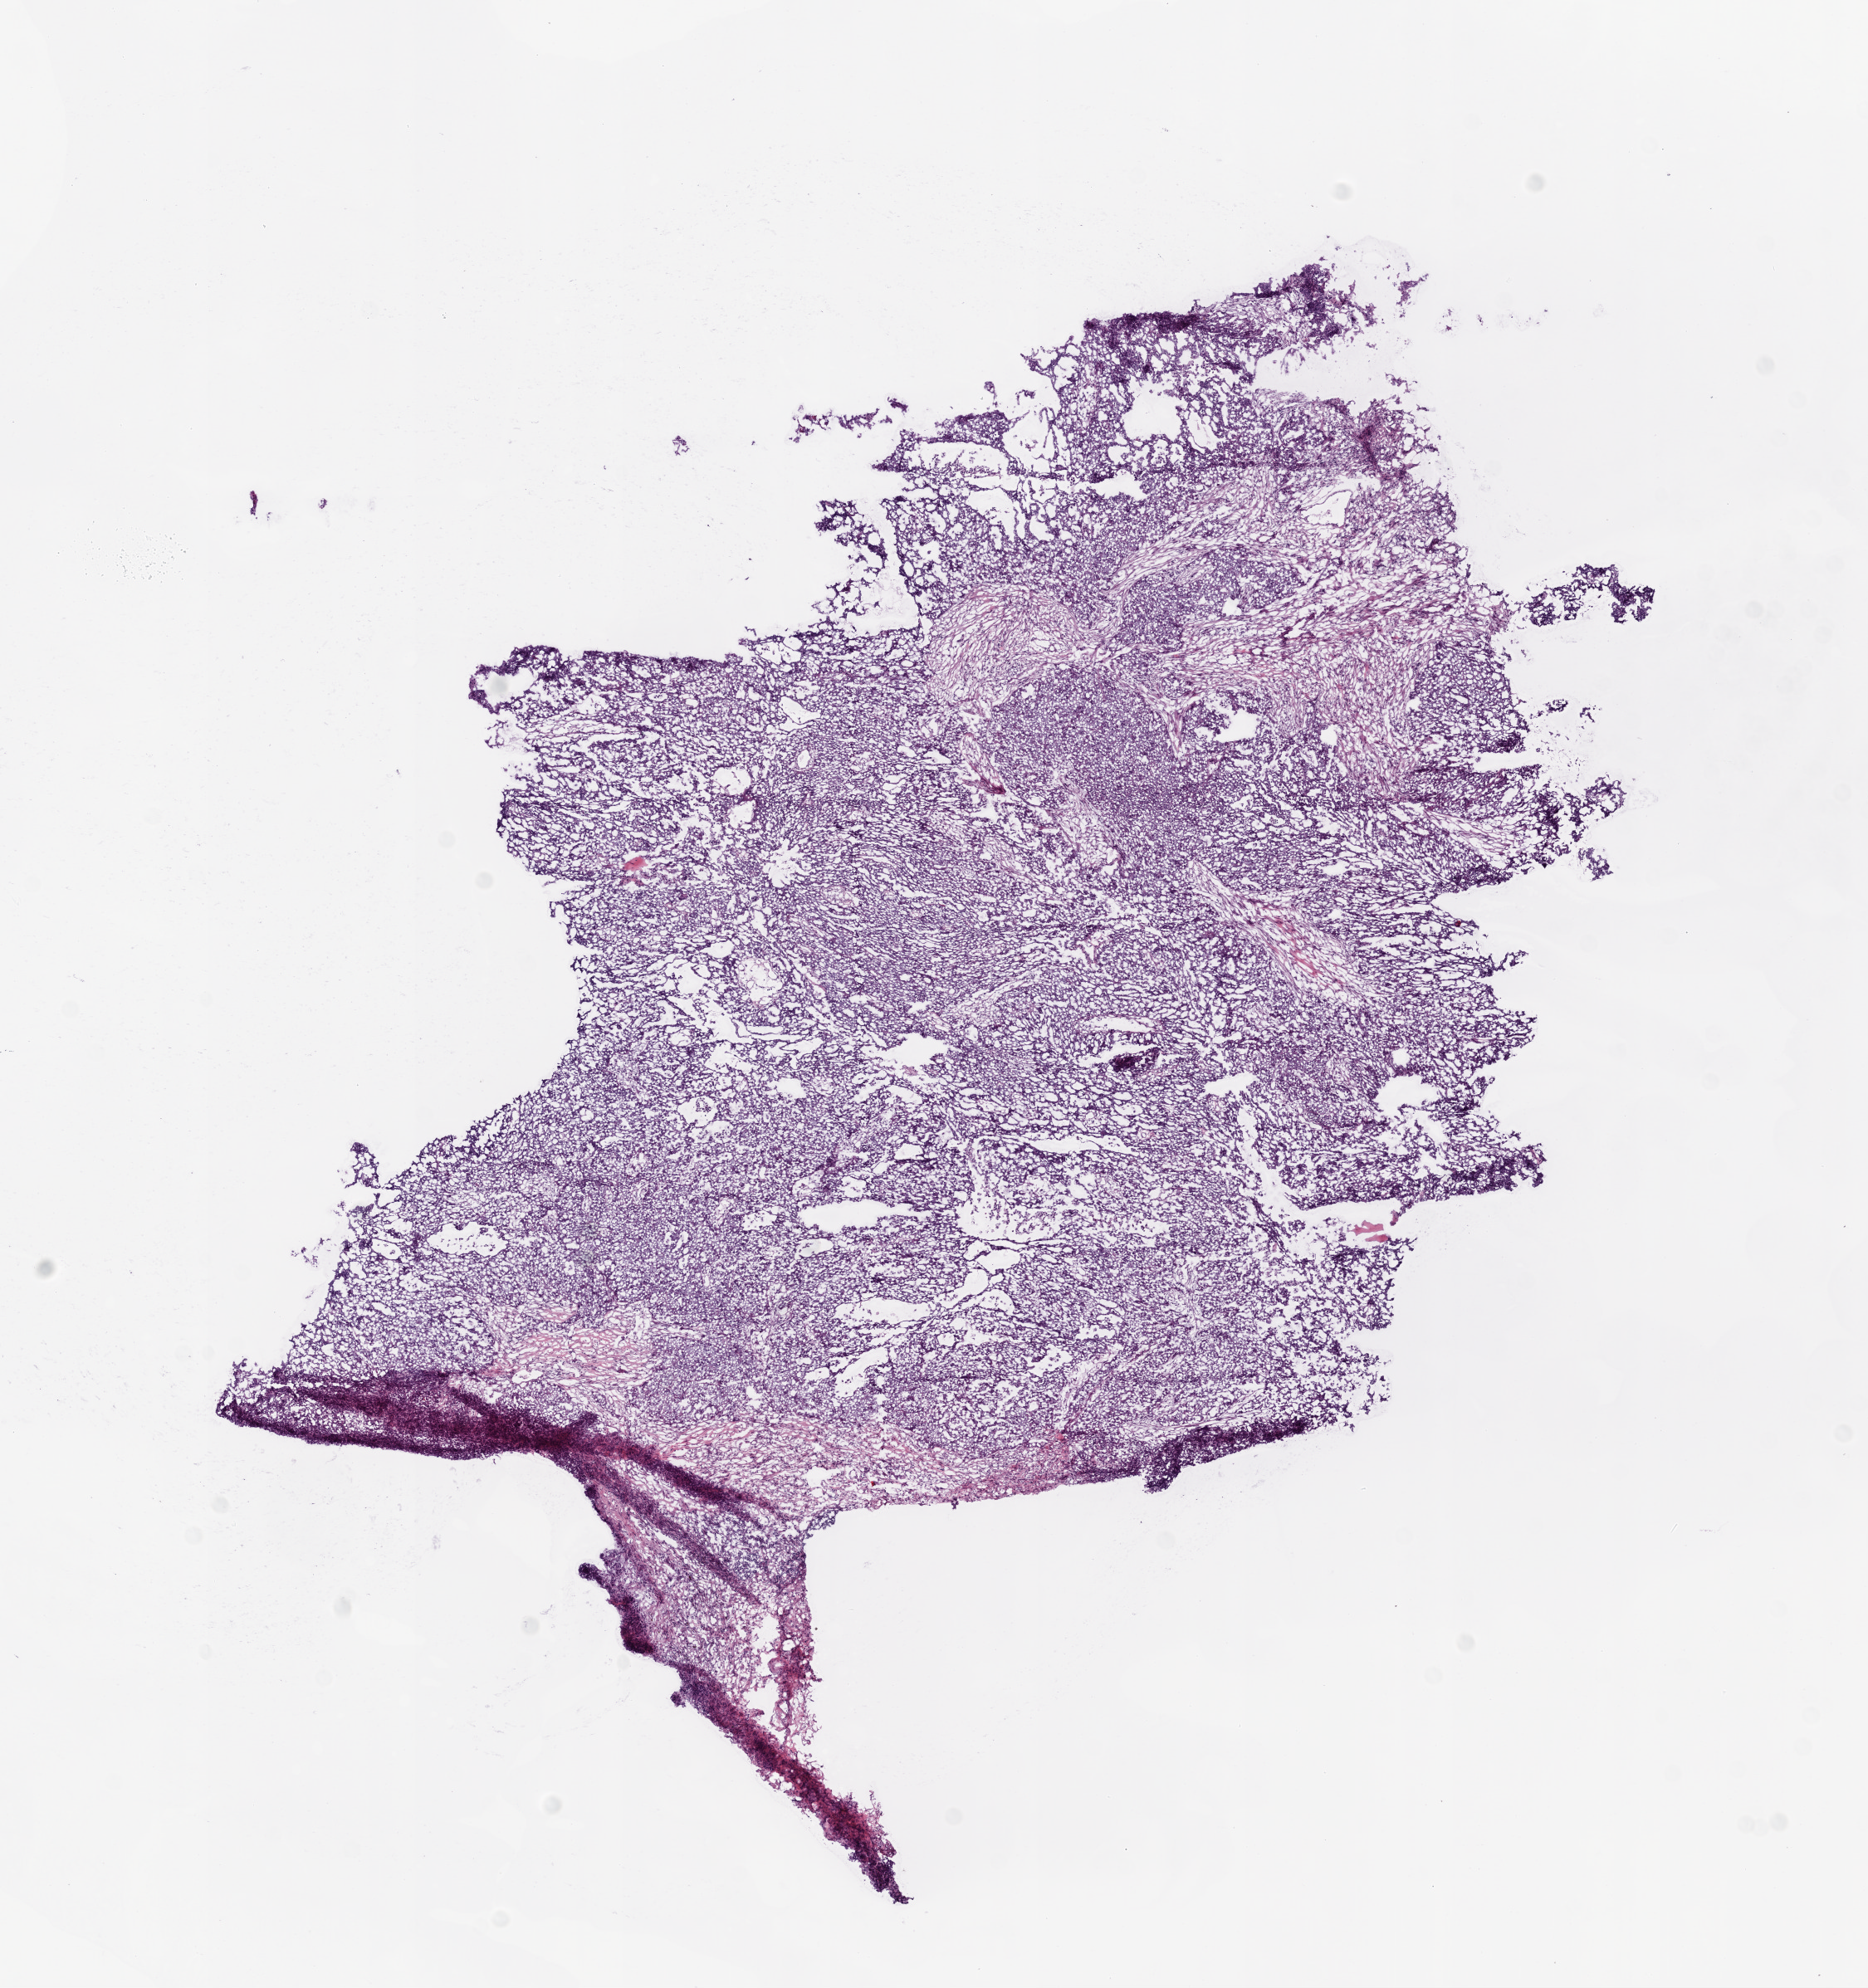
Digitized Hematoxylin and eosin (H&E) stained tissue section (whole slide) — low-resolution overview of the scanned area, about 9.0 x 9.6 mm (acquisition: 20x scan). Frozen section. Primary tumour sample from the ovary. Female, age 46 years at initial diagnosis. Histologic grade: G3 (poorly differentiated). Composition of this section per pathologist review: tumour cells 89%, tumour nuclei 90%, normal cells 0%, stromal cells 10%, necrosis 1%.
FIGO stage: IIIC. Histologic diagnosis: Serous cystadenocarcinoma, NOS. Laterality: bilateral.